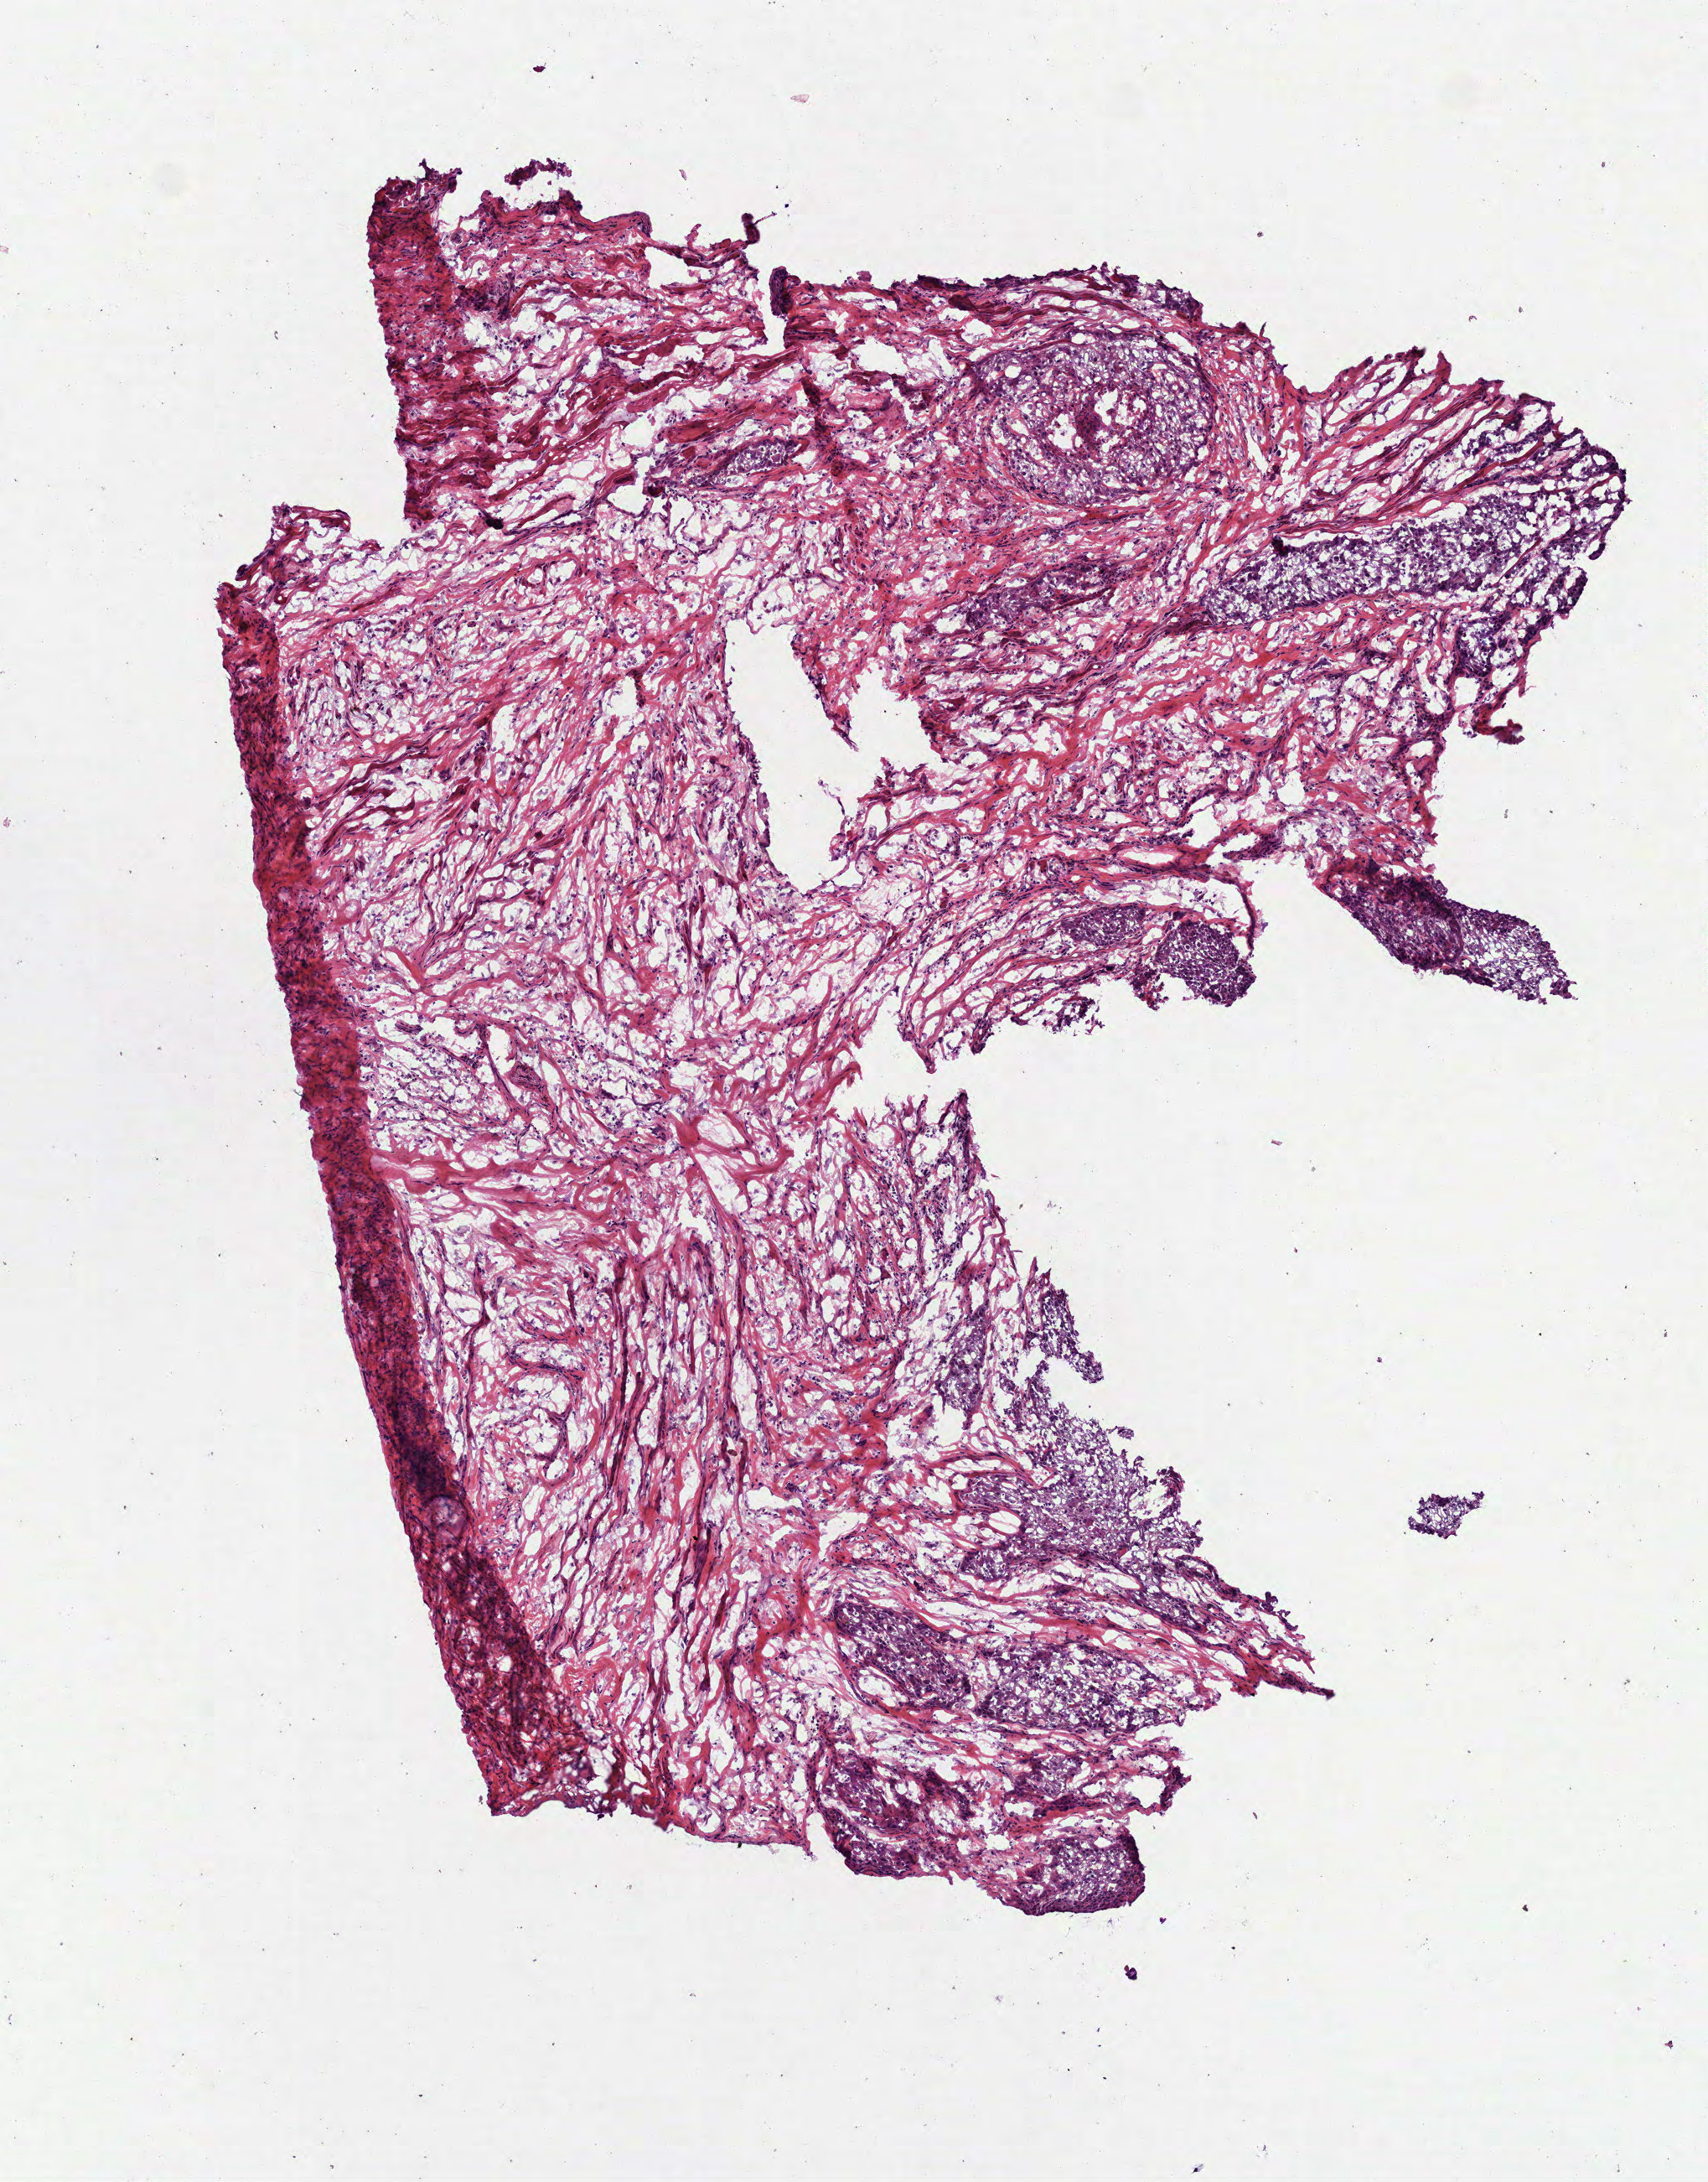
Whole-slide histology image, Hematoxylin and eosin (H&E) stained — whole scanned area (about 4.1 x 5.2 mm, slide scanned at 40x) shown as a low-resolution overview, frozen section, primary tumour sample from the head and neck. Male, age 61 years at initial diagnosis. Histologic grade: G3 (poorly differentiated). Pathologist review of this section (percent, as recorded): tumour cells 60%, tumour nuclei 60%, normal cells 0%, stromal cells 38%, necrosis 2%. Infiltration values recorded for this section: lymphocyte infiltration 5%, monocyte infiltration 0%, neutrophil infiltration 6%.
* pathologic diagnosis: Squamous cell carcinoma, NOS (tongue, NOS)
* AJCC pathologic stage: II (7th edition)